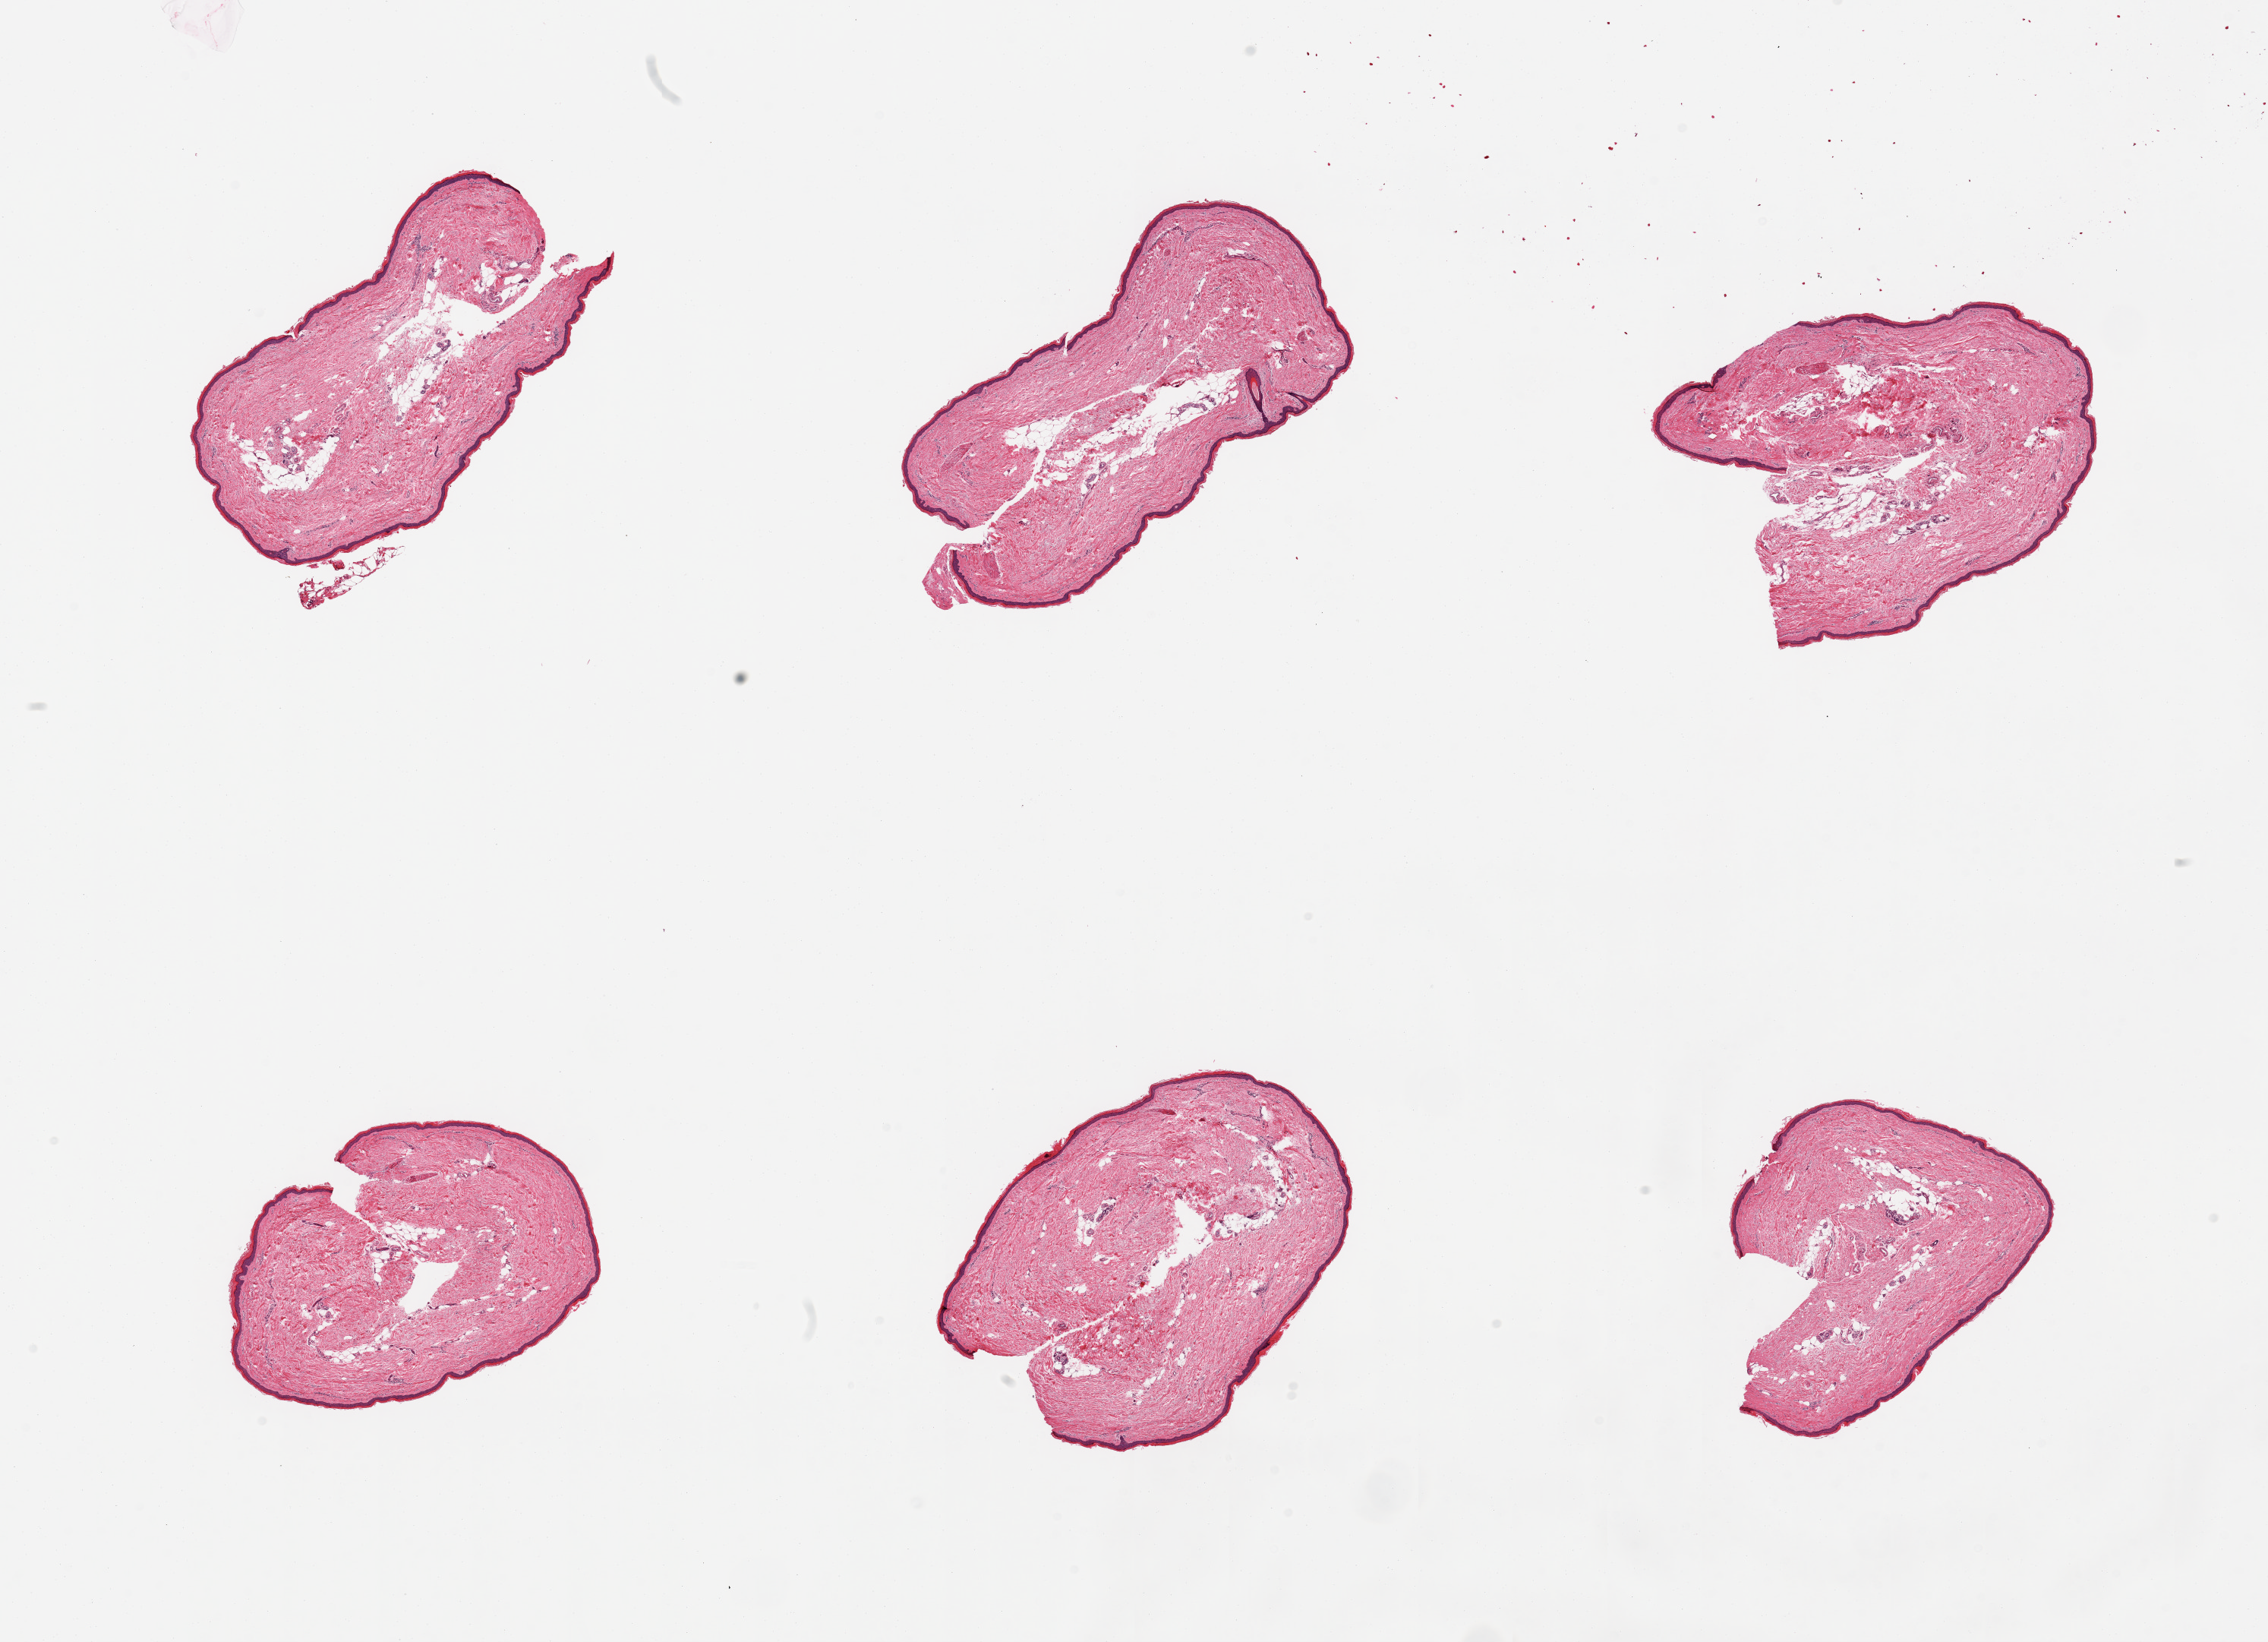
Whole-slide image, H&E stain, brightfield, a low-resolution overview of the entire scanned area, about 23.6 x 17.1 mm. PAXgene-fixed, paraffin-embedded tissue. Section of skin of lower leg (target tissue). Tissue donor sample. Donor: female.
• review note (as recorded): 6 pieces; well trimmed, <10% internal fat, epidermis measures 34 microns